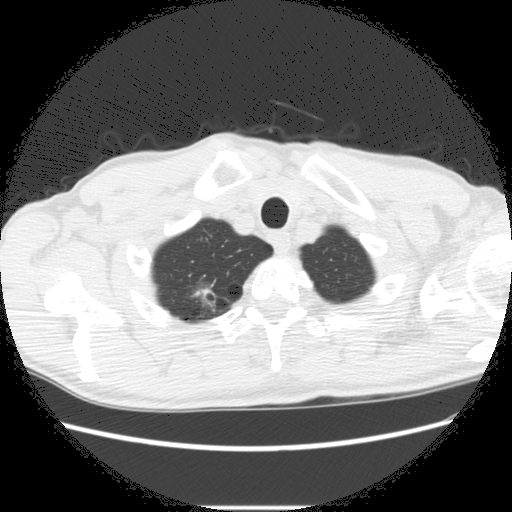
Chest CT (low-dose screening protocol), one axial image, second screening round (one year after baseline), lung window (W 1500 / L -600 HU), 2.5 mm slice thickness, 120 kVp, 512 × 512 image matrix, field of view 360 × 360 mm. Male, age 66 years at enrolment. Former smoker at enrolment.
Expert-annotated lung lesion, box from (x=171, y=276) to (x=235, y=327) px. The screening reader recorded 5 non-calcified nodules or masses ≥4 mm on this exam (right lower lobe, right upper lobe, right upper lobe, right upper lobe, left lower lobe); which of them this box marks is not recorded. Lung cancer was diagnosed 75 days after this screen: adenocarcinoma, NOS, right upper lobe, undifferentiated (G4), stage IA (AJCC 6th edition), 20 mm at pathology.